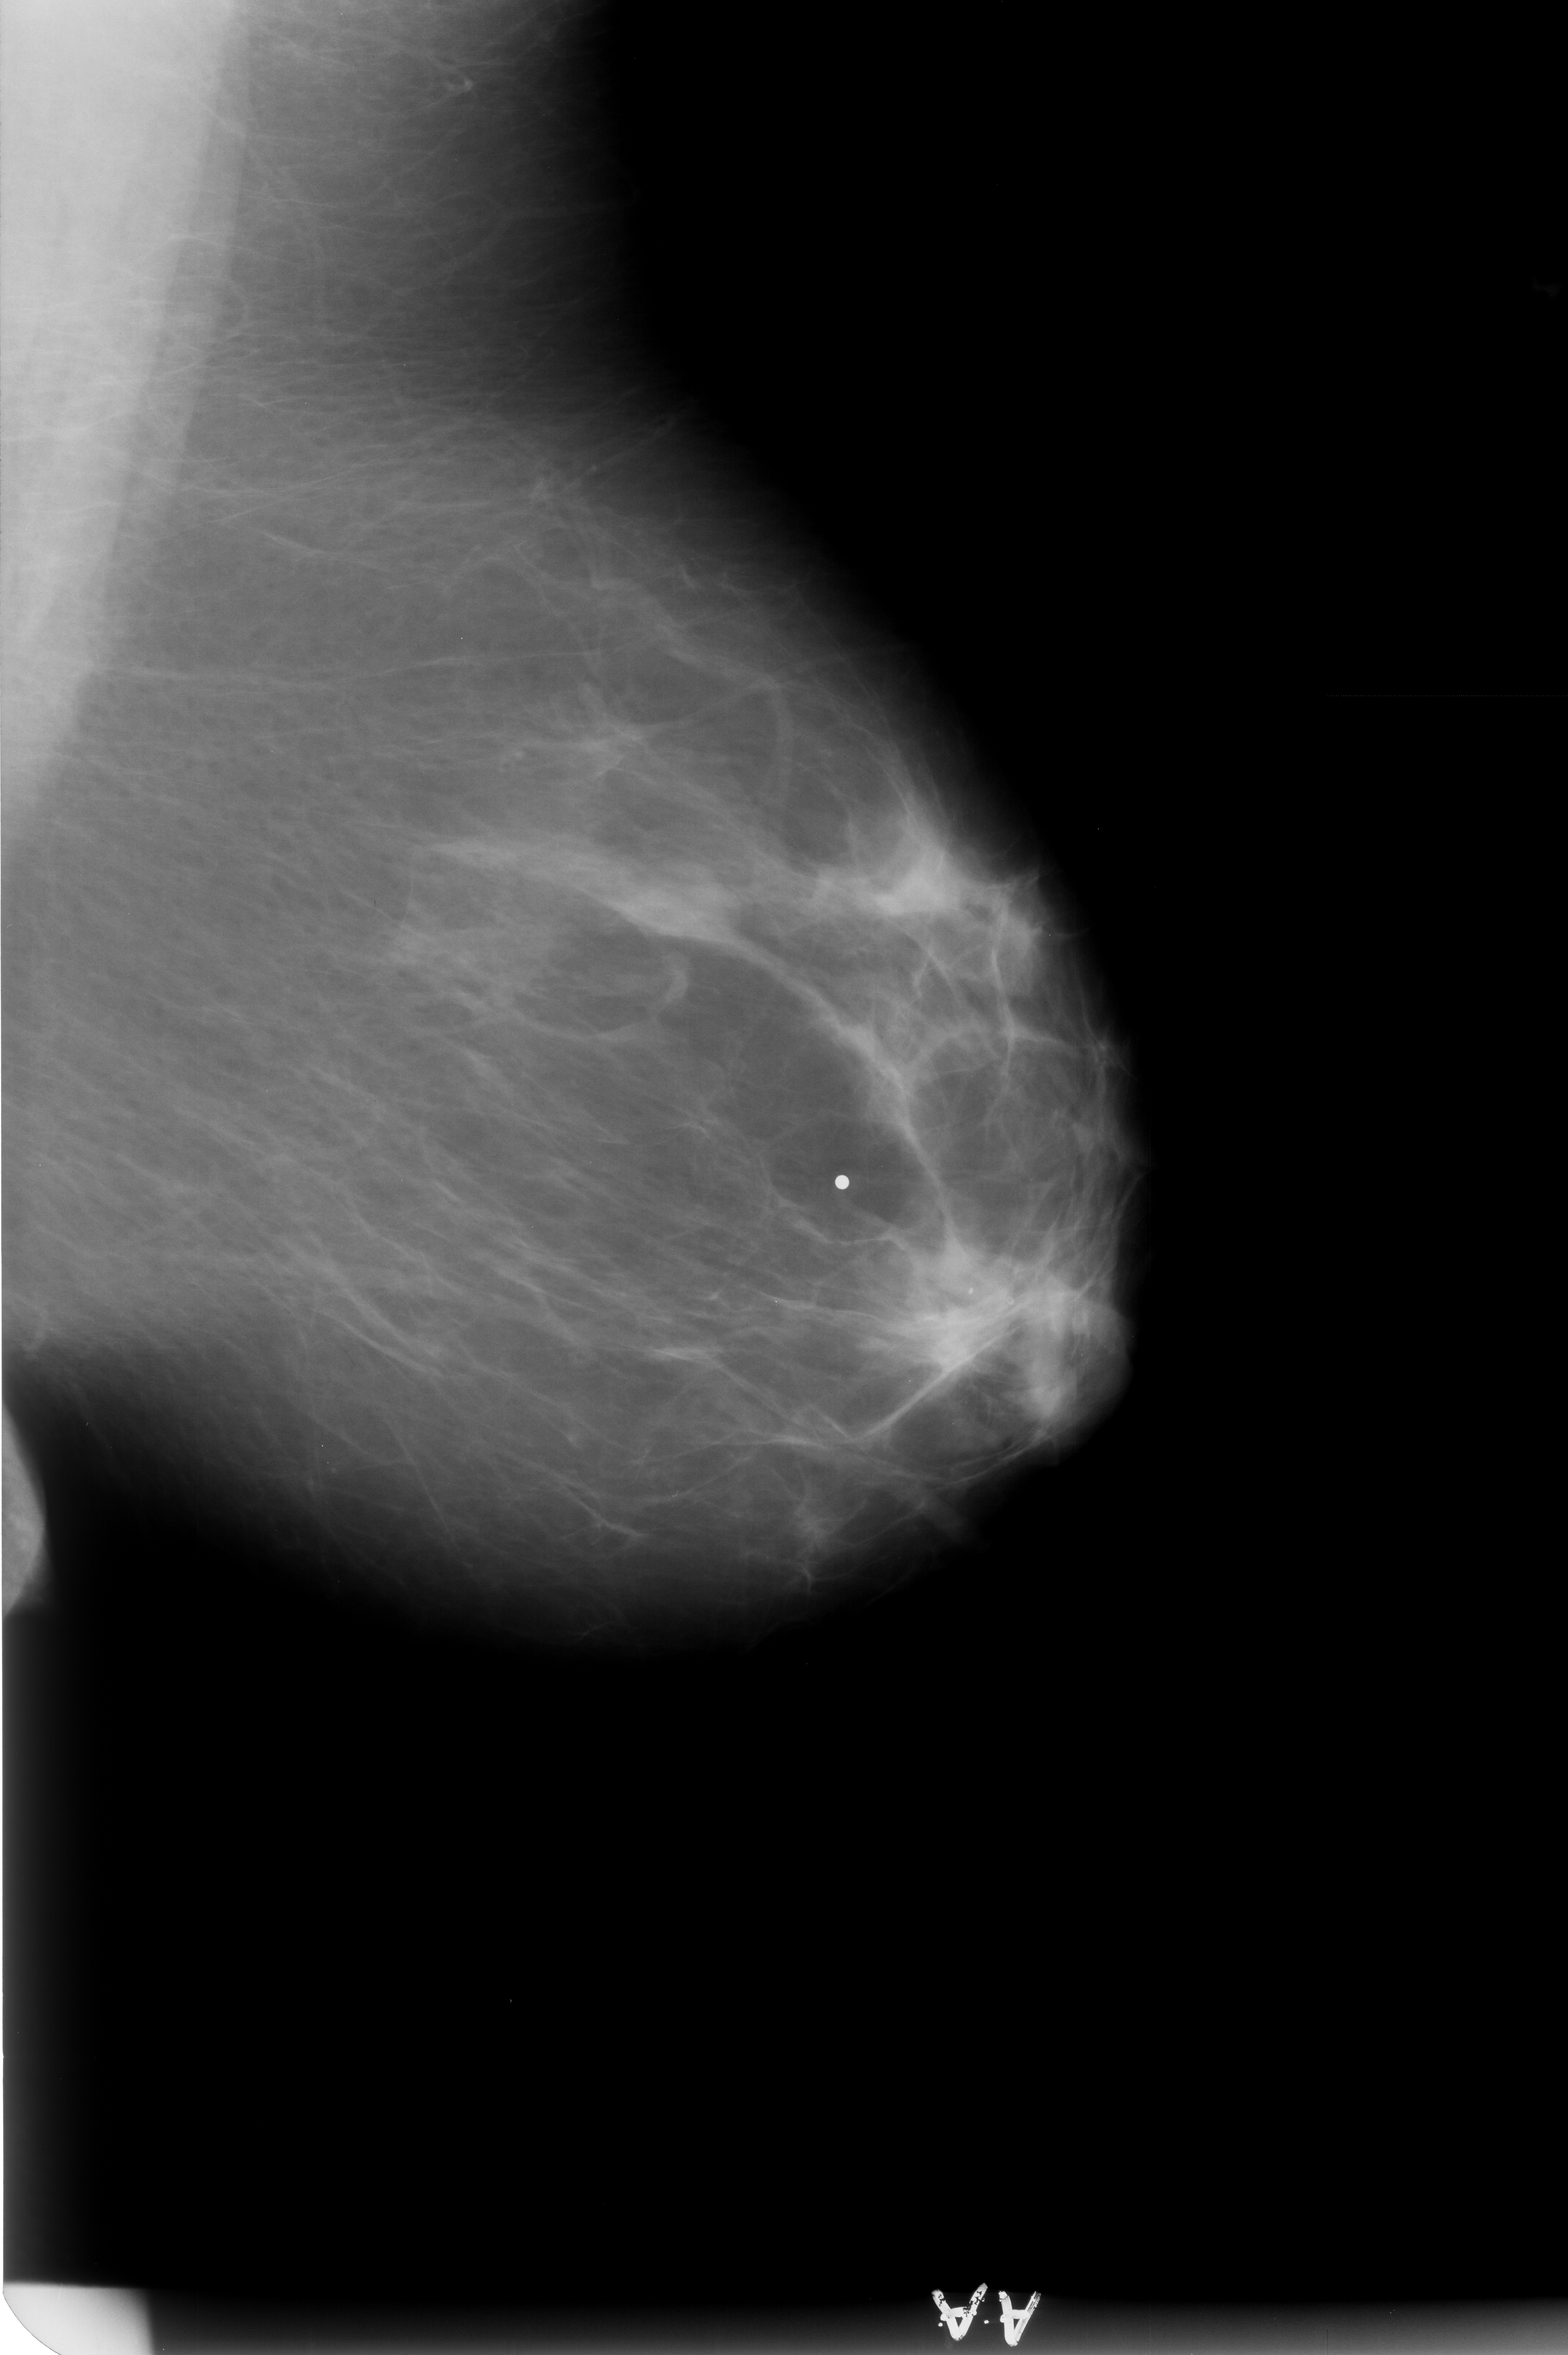
Mammogram (digitized film); left breast; MLO view; breast composition: scattered fibroglandular densities (BI-RADS density category 2 of 4).
- Radiologist-marked abnormalities on this image: Finding 1 of 2: calcifications, morphology lucent center / punctate; BI-RADS assessment category 2; benign; no additional work-up was recommended (benign without callback).
- Finding 2 of 2: calcifications, morphology lucent center / punctate; BI-RADS assessment category 2; benign; no additional work-up was recommended (benign without callback).